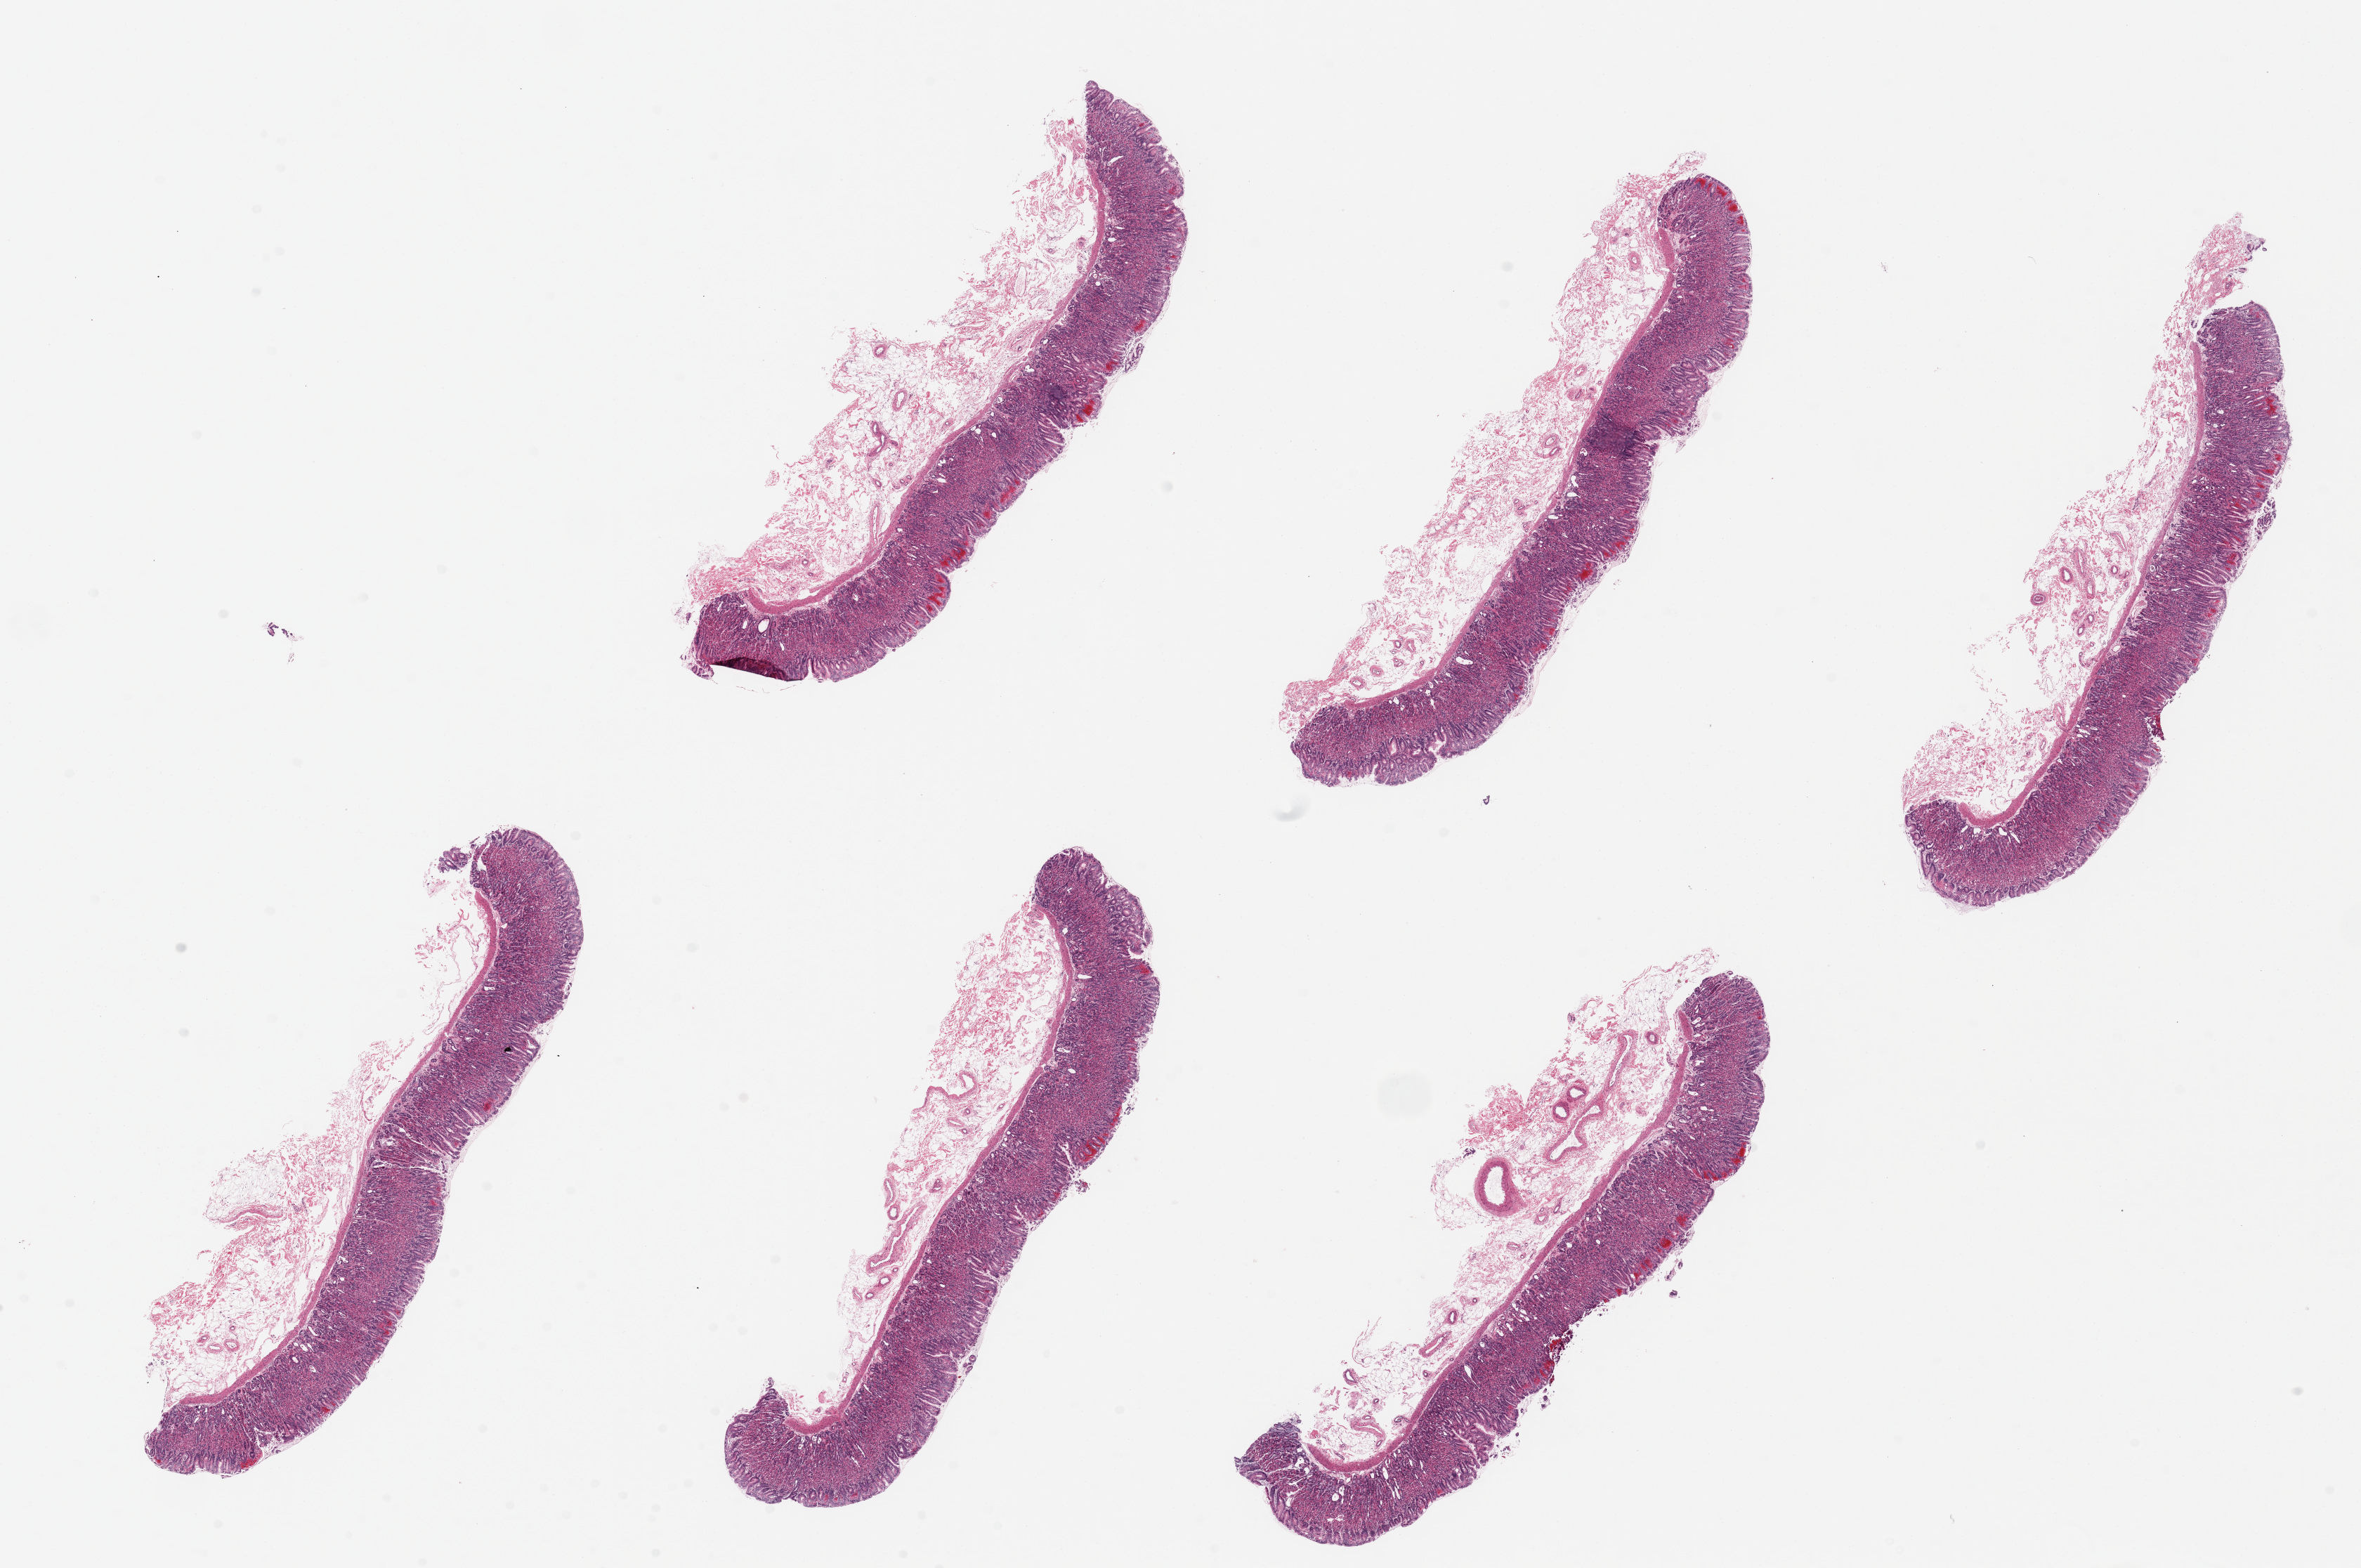
Whole-slide image, H&E stain, brightfield — shown as a low-resolution overview of the whole scanned area (about 26.6 x 17.7 mm). PAXgene-fixed, paraffin-embedded tissue. Sampled site (target tissue): stomach. Donor tissue sample. Donor: male.
• review note (as recorded): 6 pieces ~8x2mm ~50% mucosa, reasonably well preserved